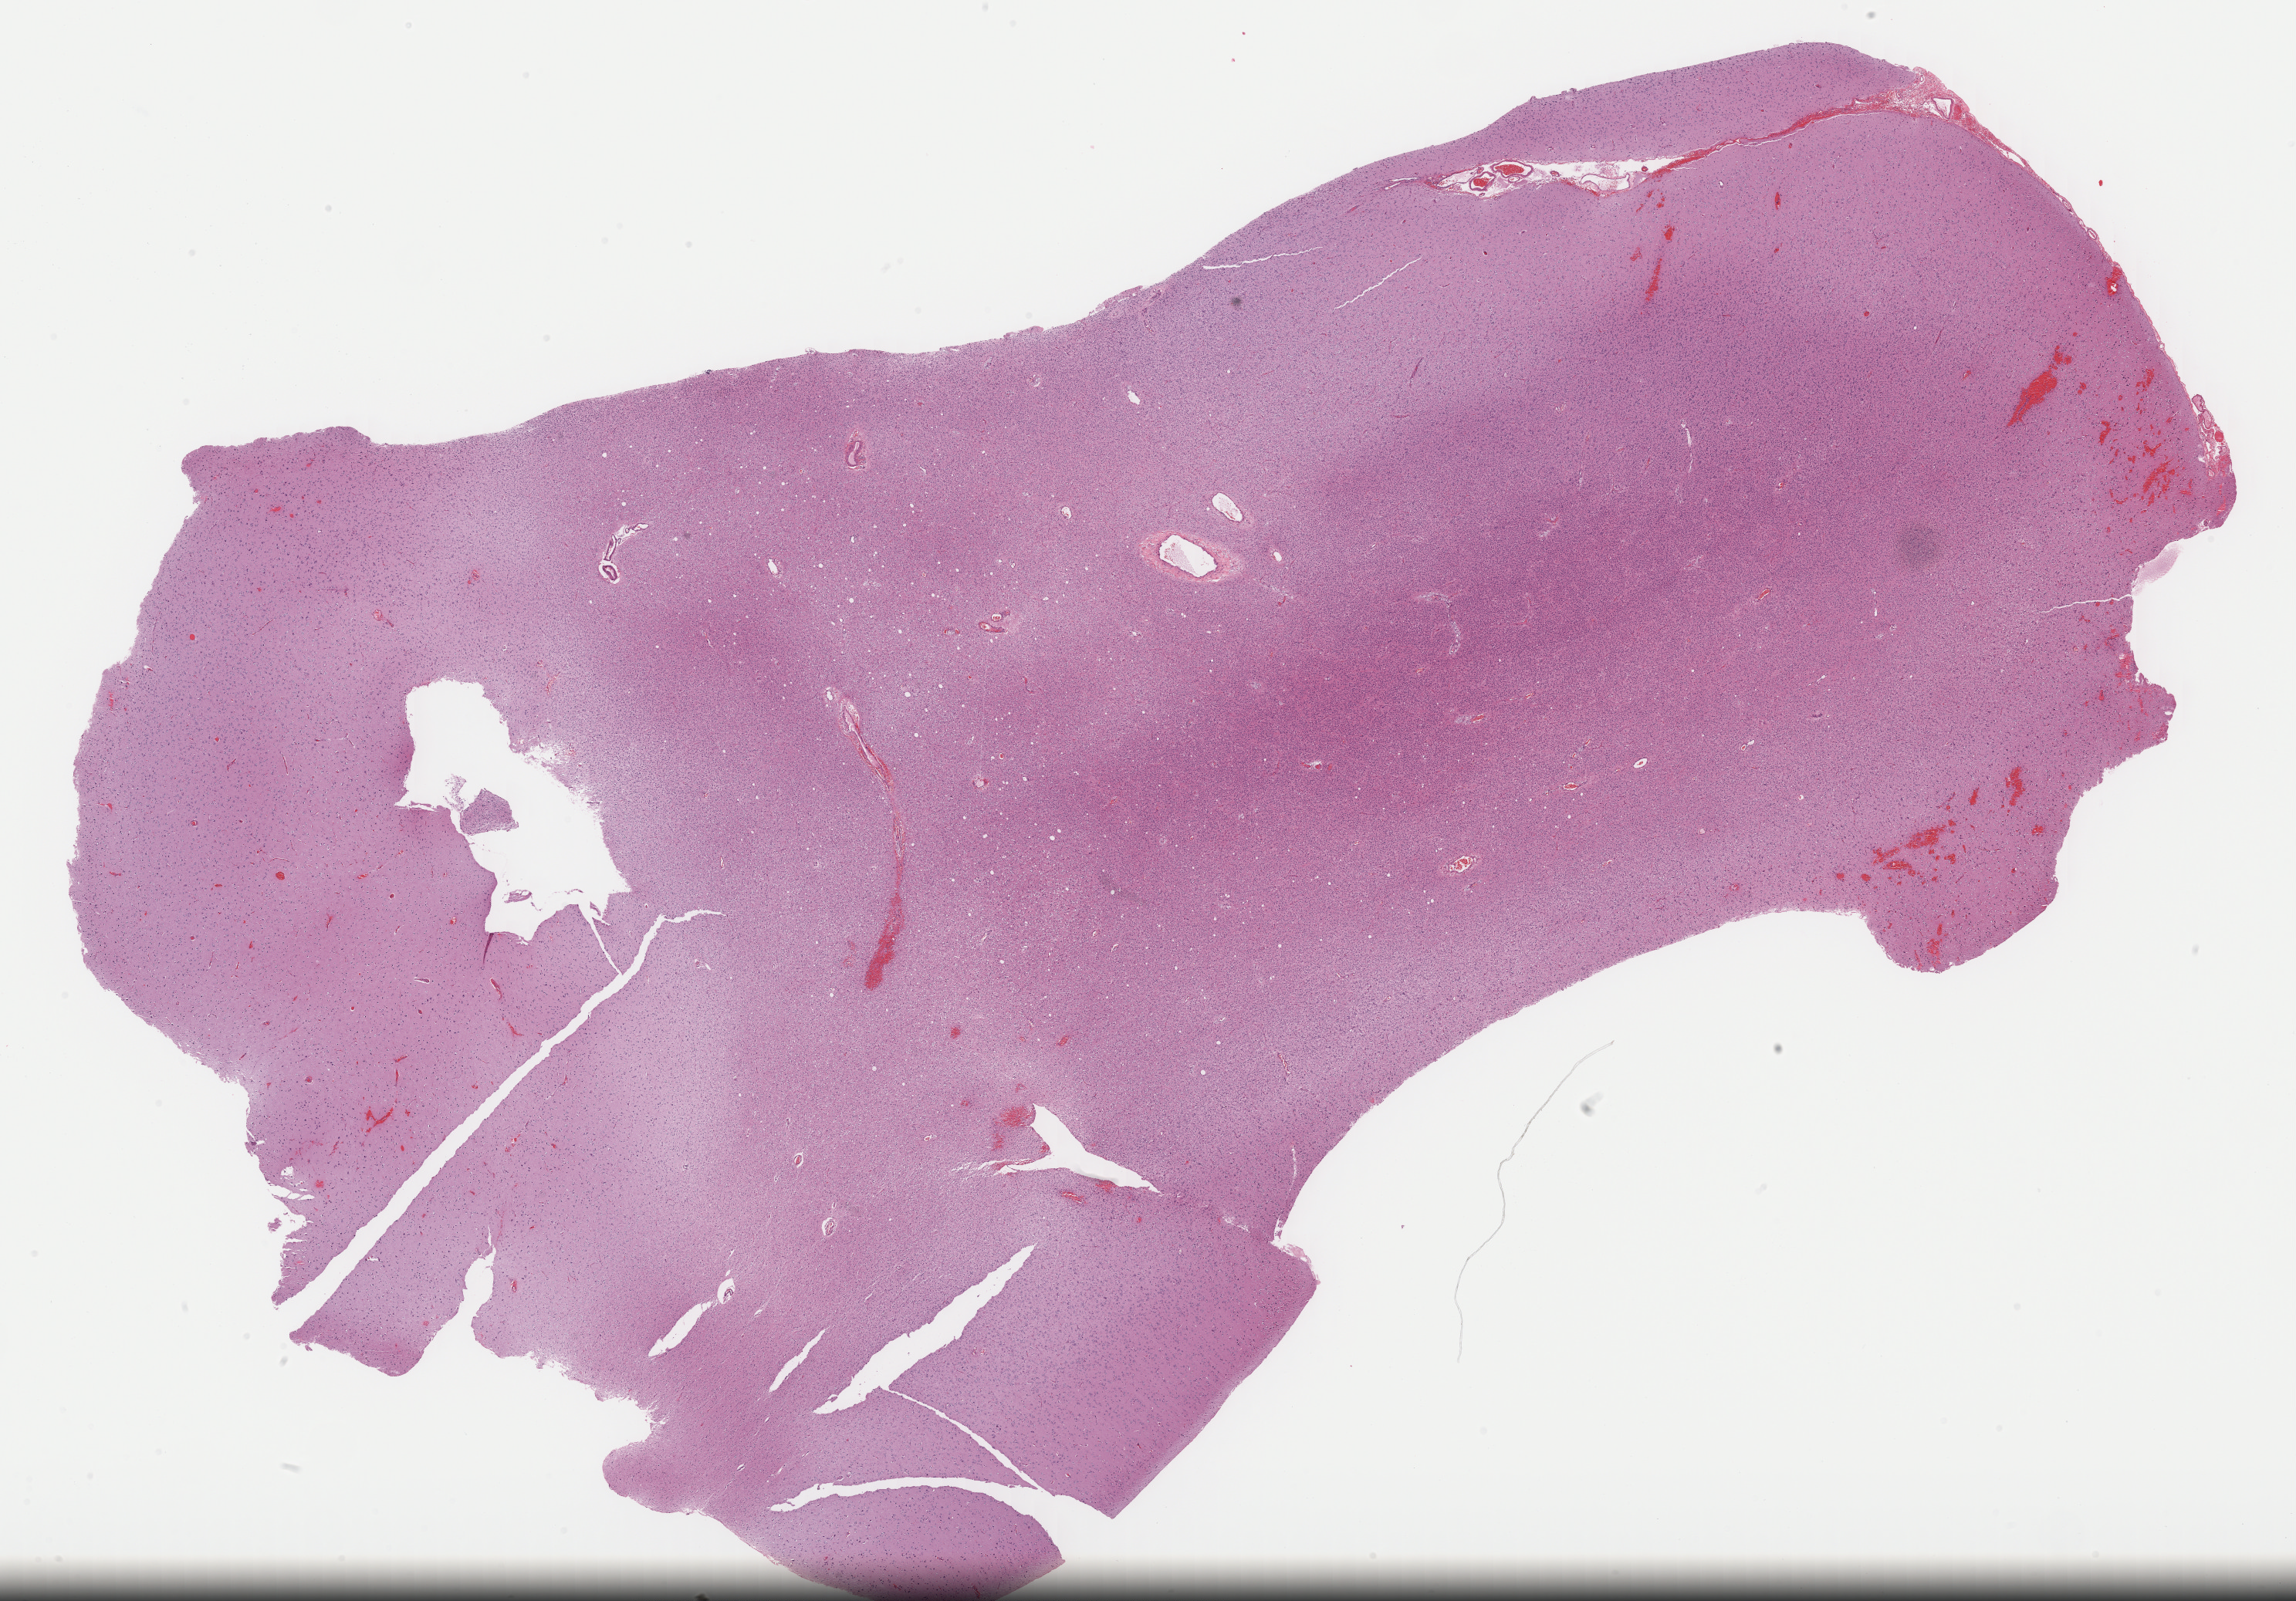
Digitized Hematoxylin and eosin (H&E) stained tissue section (whole slide) — a low-resolution overview of the entire scanned area, about 23.4 x 16.3 mm (slide scanned at 40x). Formalin-fixed paraffin-embedded (FFPE) diagnostic section. Sample: primary tumour, brain. Patient: male, age at initial diagnosis 17 years. Histologic grade: G2 (moderately differentiated).
• laterality: left
• pathologic diagnosis: Oligodendroglioma, NOS (cerebrum)